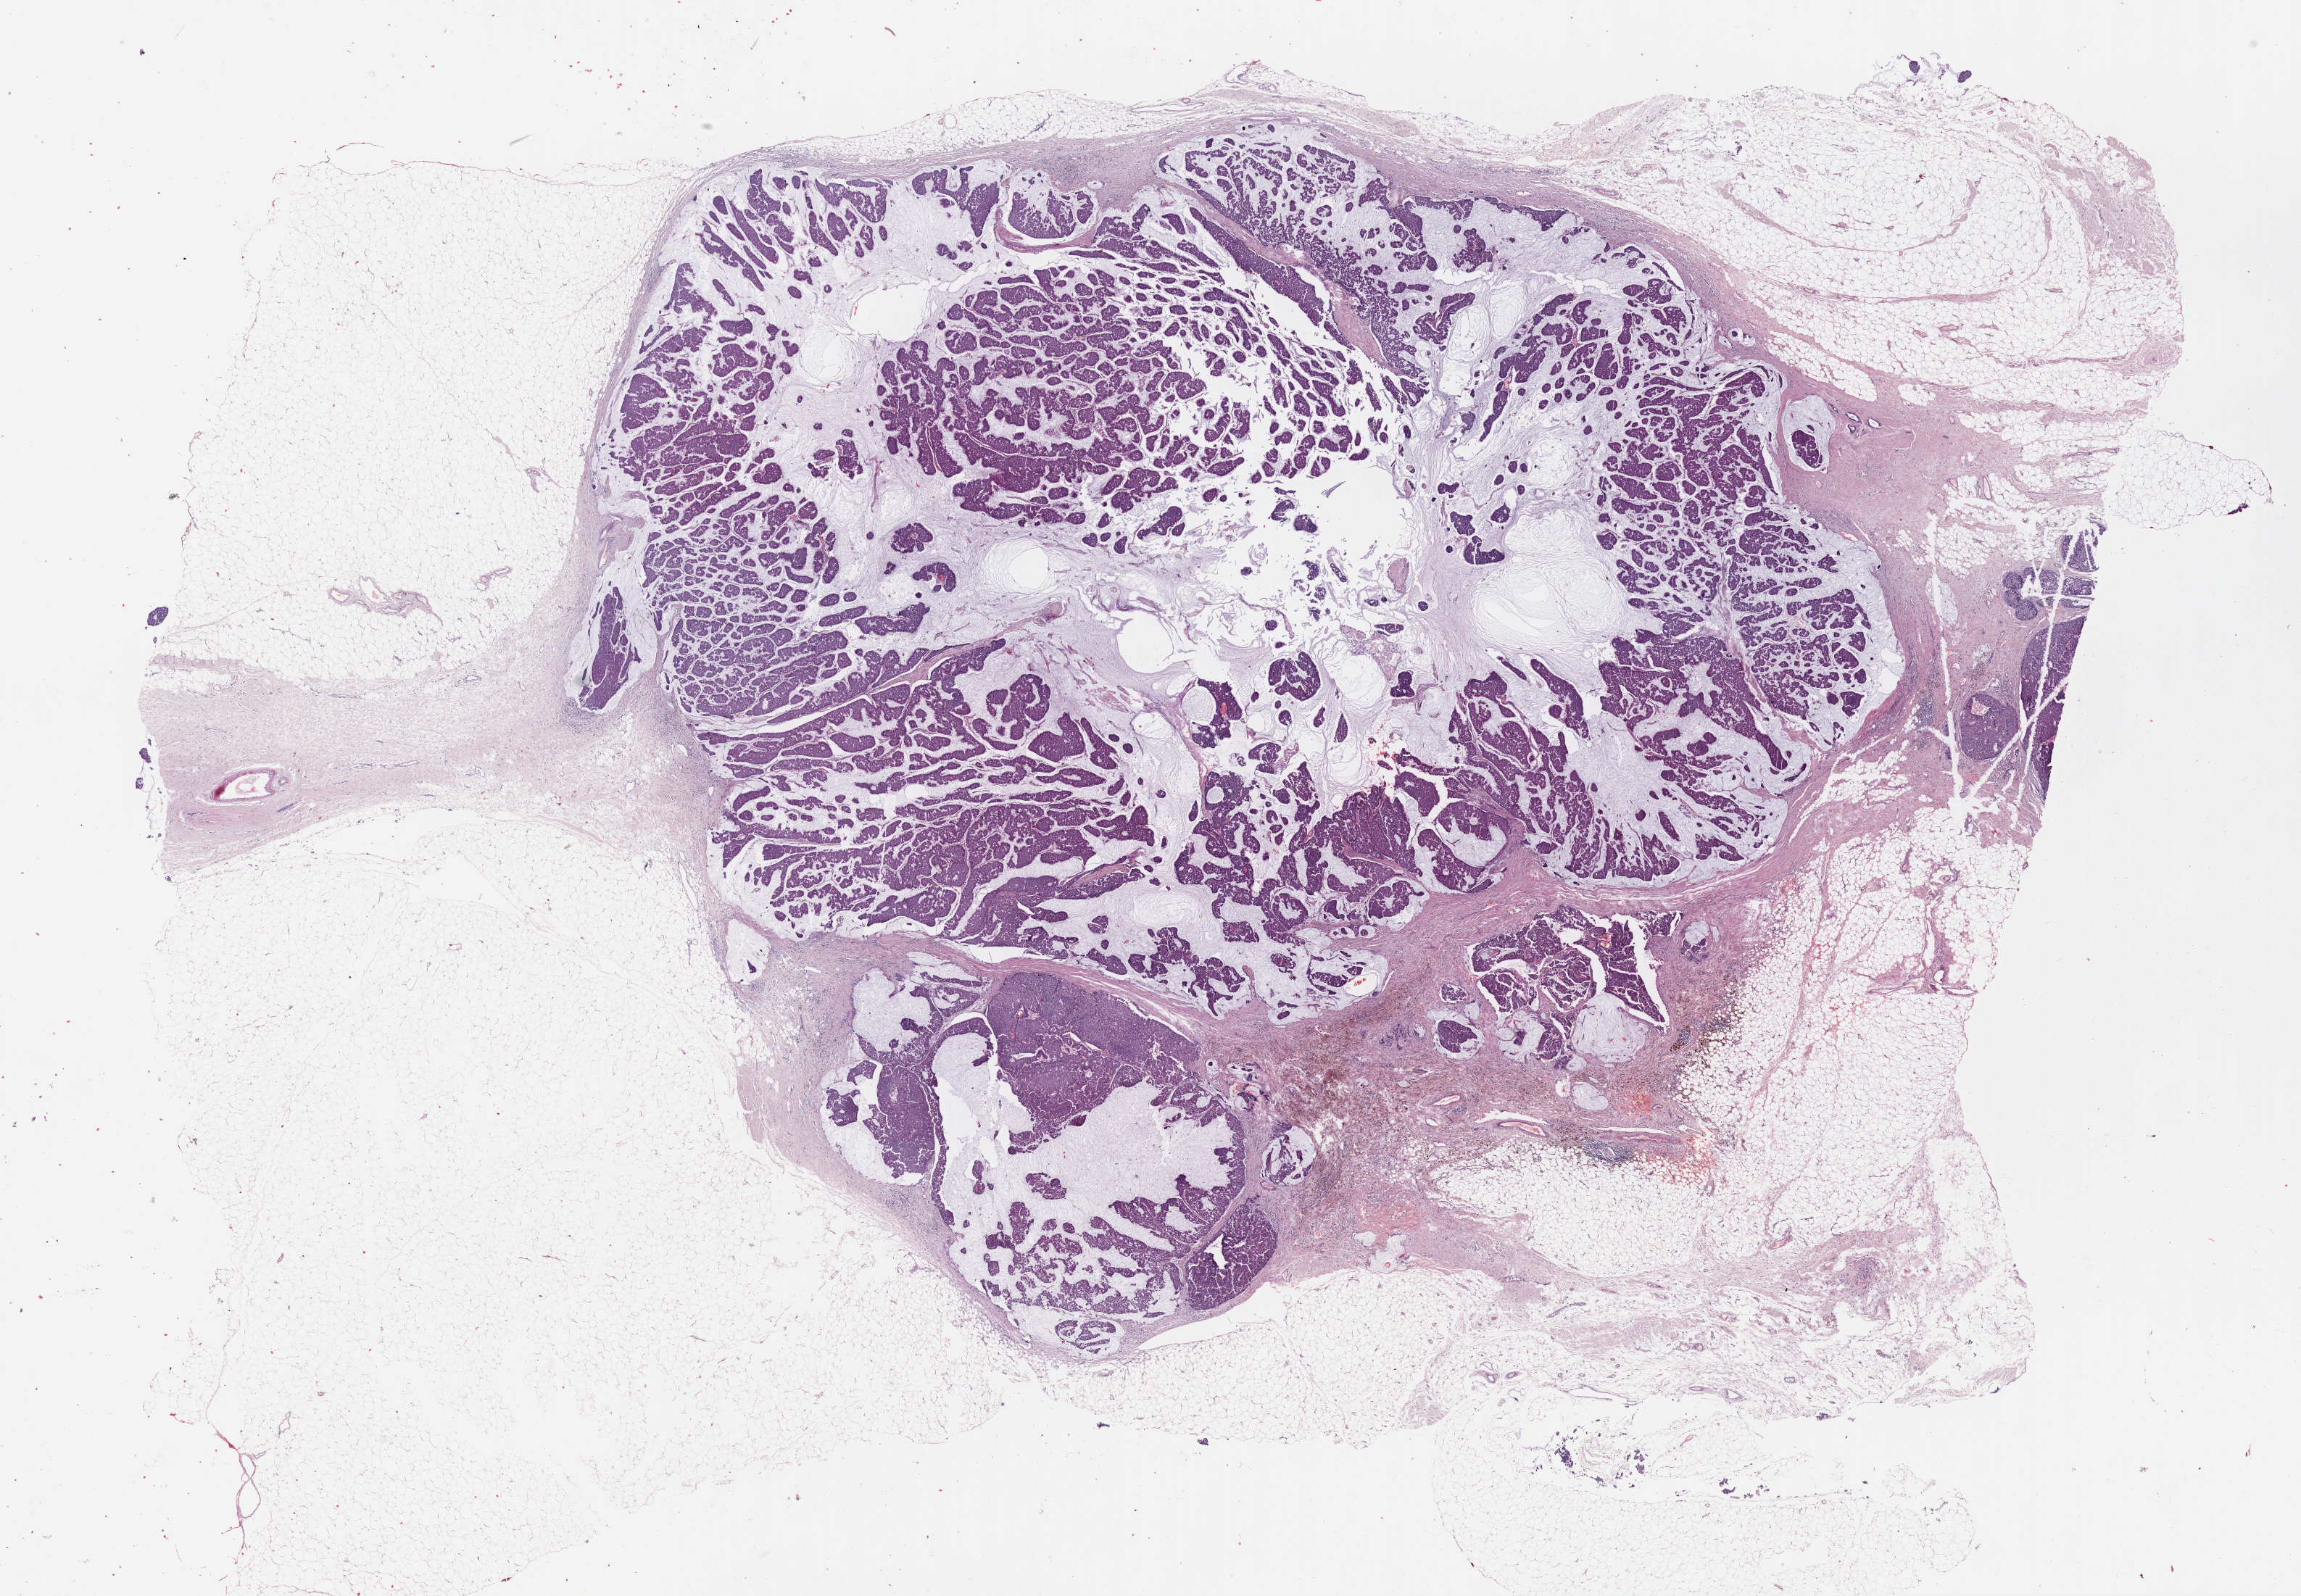
Digitized Hematoxylin and eosin (H&E) stained tissue section (whole slide), low-resolution overview of the scanned area, about 25.7 x 17.8 mm, formalin-fixed paraffin-embedded (FFPE) diagnostic section, sample: primary tumour, breast. Female, age 84 years at initial diagnosis.
Diagnosis: Mucinous adenocarcinoma.